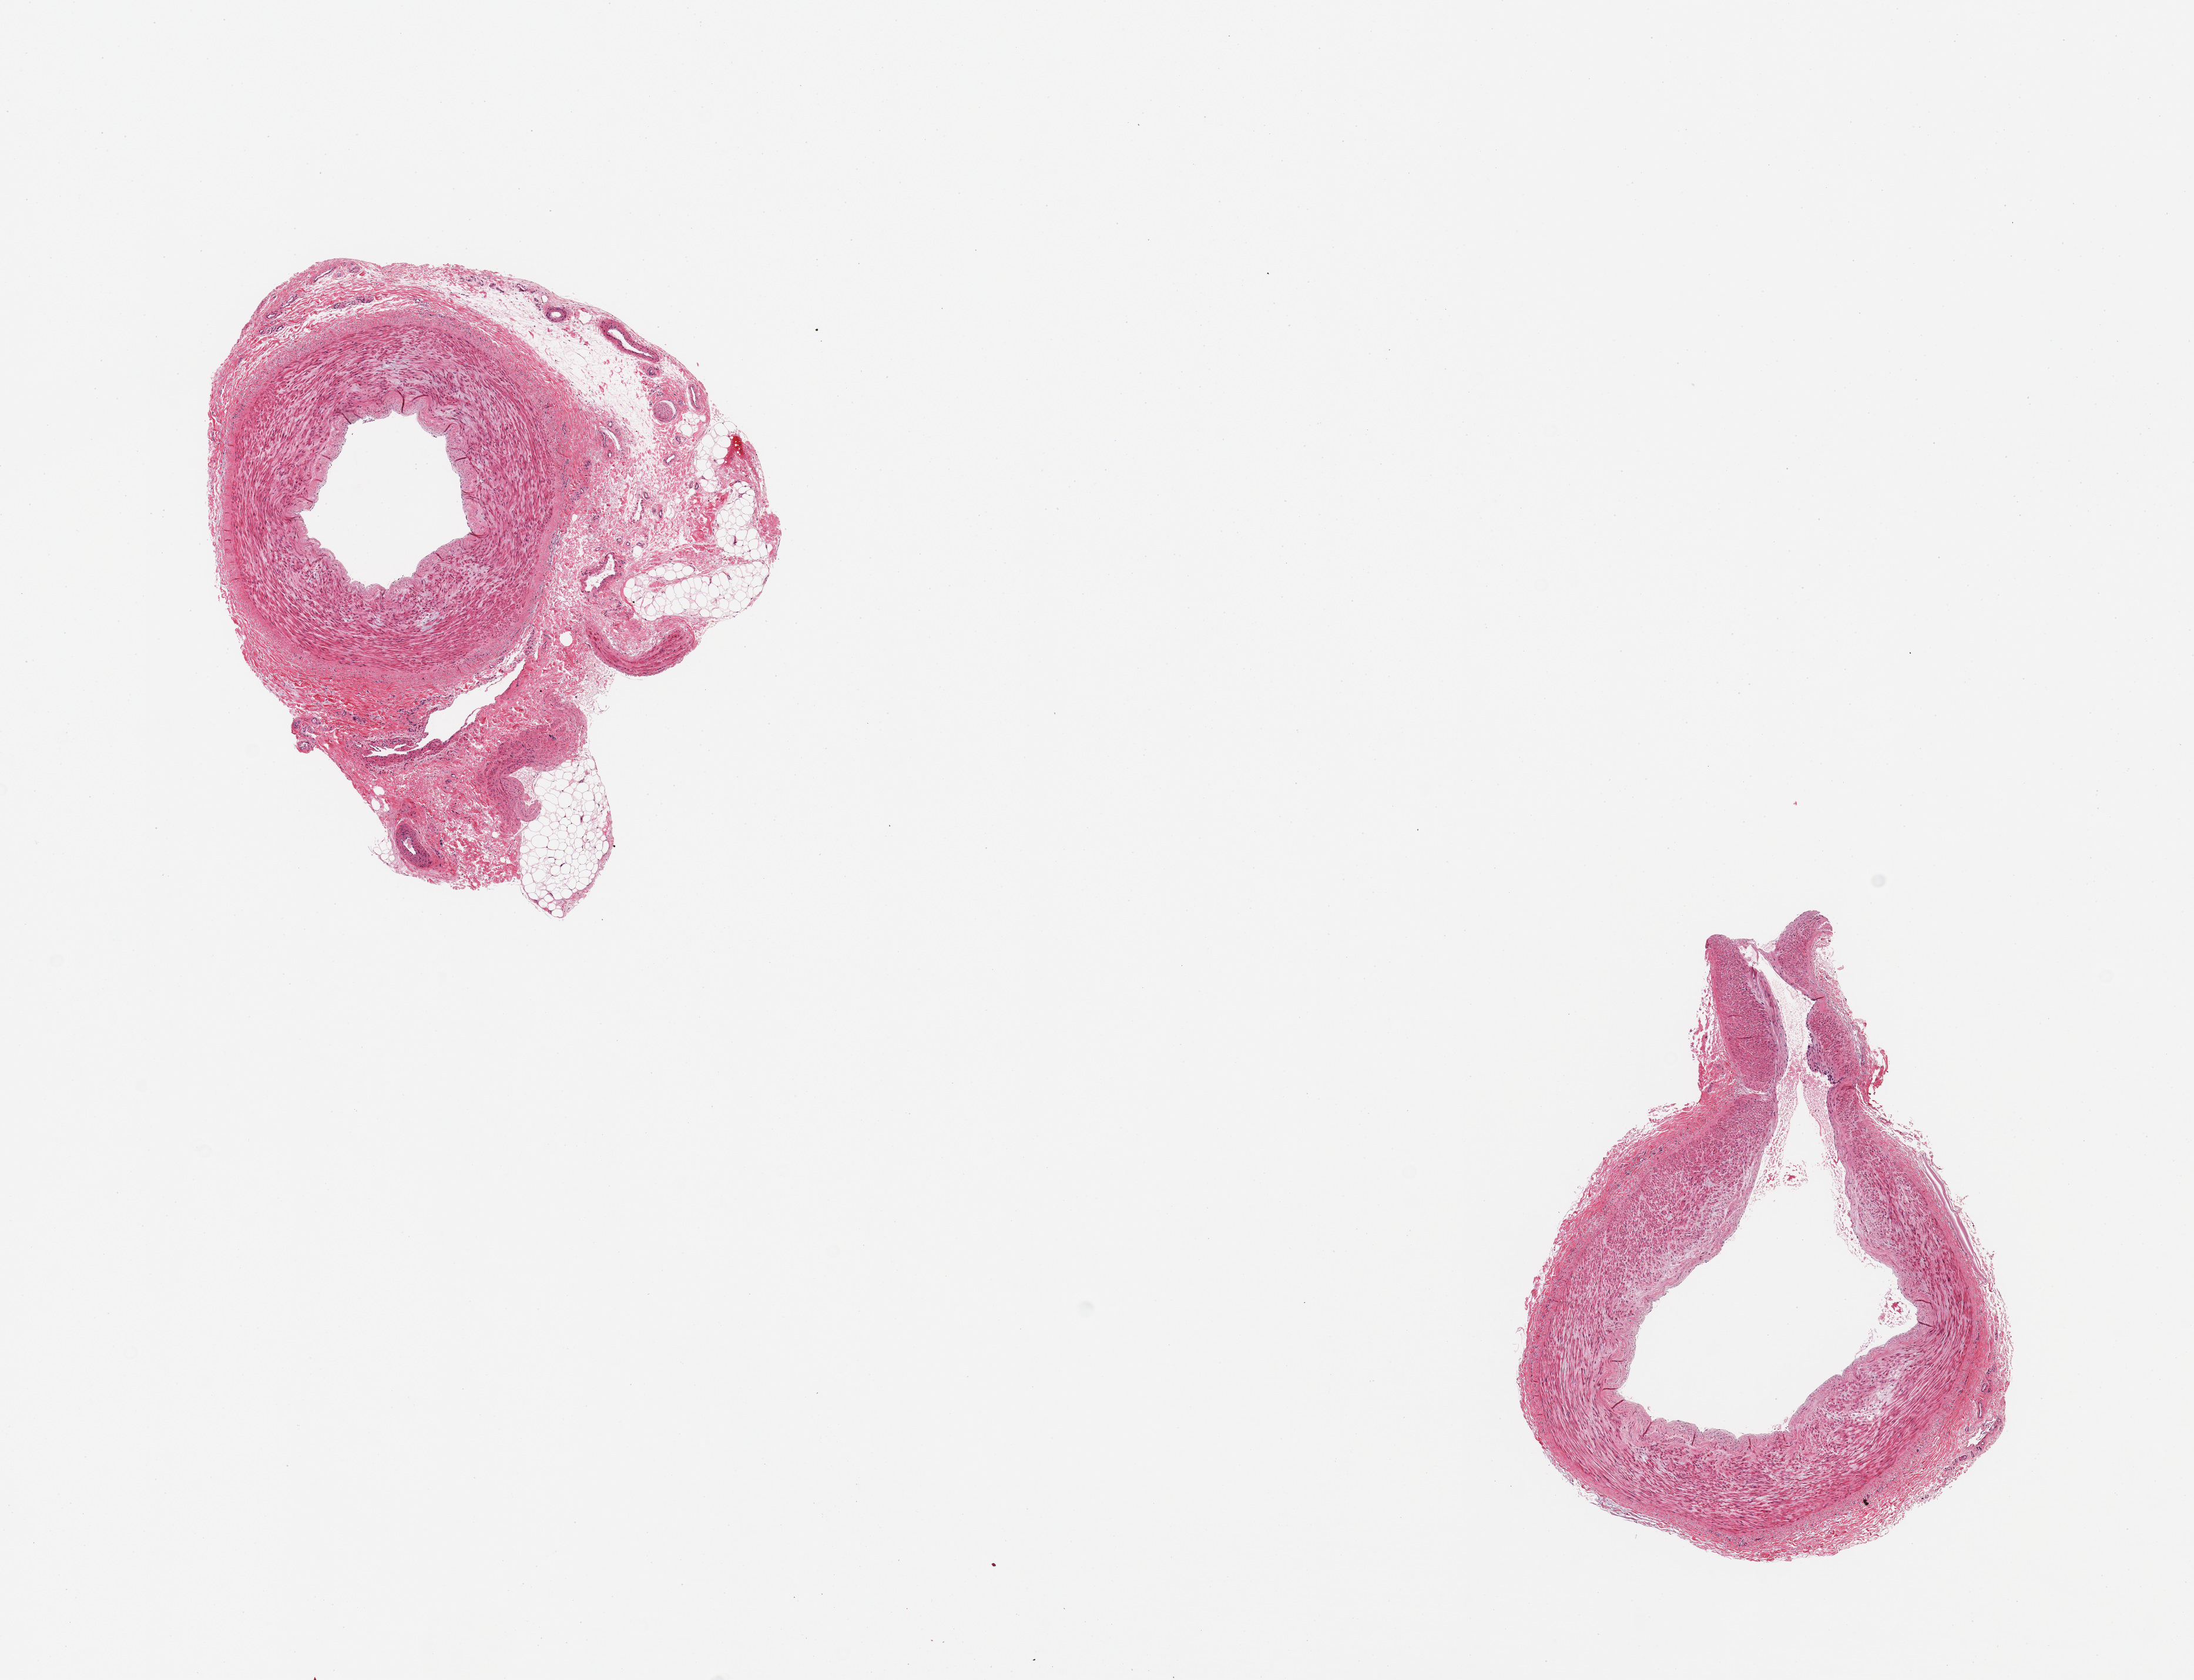
Digitized H&E-stained section, low-resolution overview of the scanned area, about 14.8 x 11.3 mm. PAXgene-fixed paraffin-embedded (PFPE) section. Sampled site (target tissue): tibial artery. Donor tissue sample. Donor: male.
Pathologist's review note for this sample: 2 pieces; 1 piece has partial rim of attached fat/fibrovascular tissue/nerve (~40%).